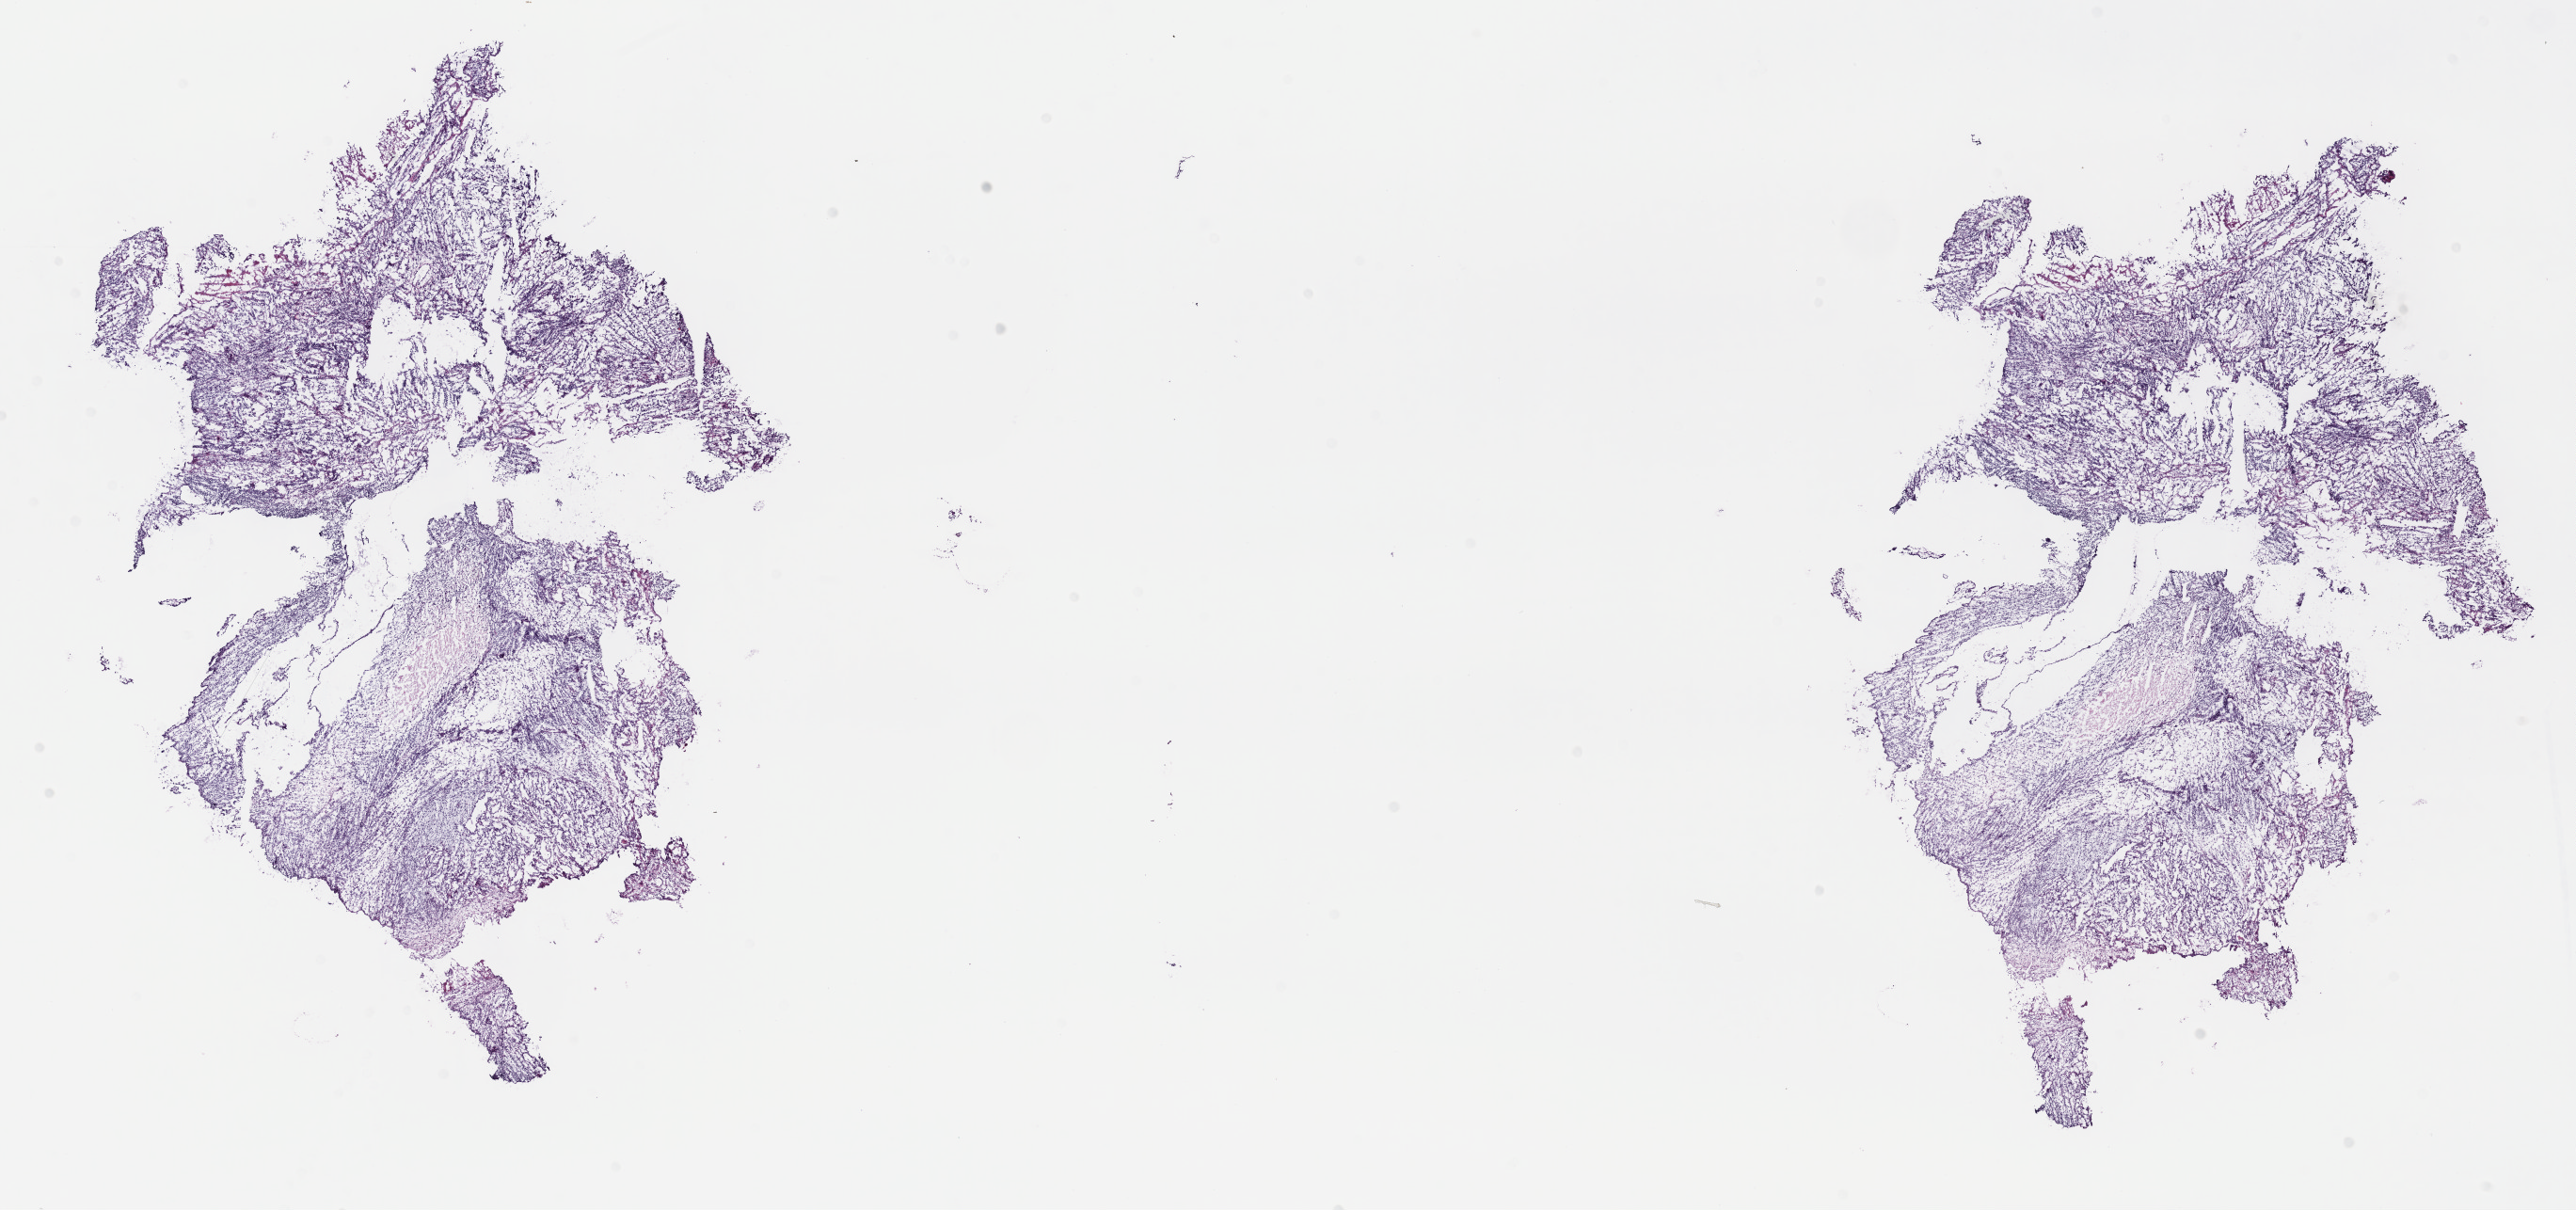
Digitized Hematoxylin and eosin (H&E) stained tissue section (whole slide) — whole scanned area (about 22.1 x 10.4 mm, from a 40x scan) shown as a low-resolution overview; frozen section; sample: primary tumour, testis. Male, age 34 years at initial diagnosis. Pathologist review of this section (percent, as recorded): tumour cells 93%, tumour nuclei 80%, normal cells 0%, stromal cells 0%, necrosis 7%. Infiltration values recorded for this section: lymphocyte infiltration 2%, monocyte infiltration 0%, neutrophil infiltration 0%.
Pathologic diagnosis: Mixed germ cell tumor. Laterality: left. AJCC pathologic stage: II (4th edition).